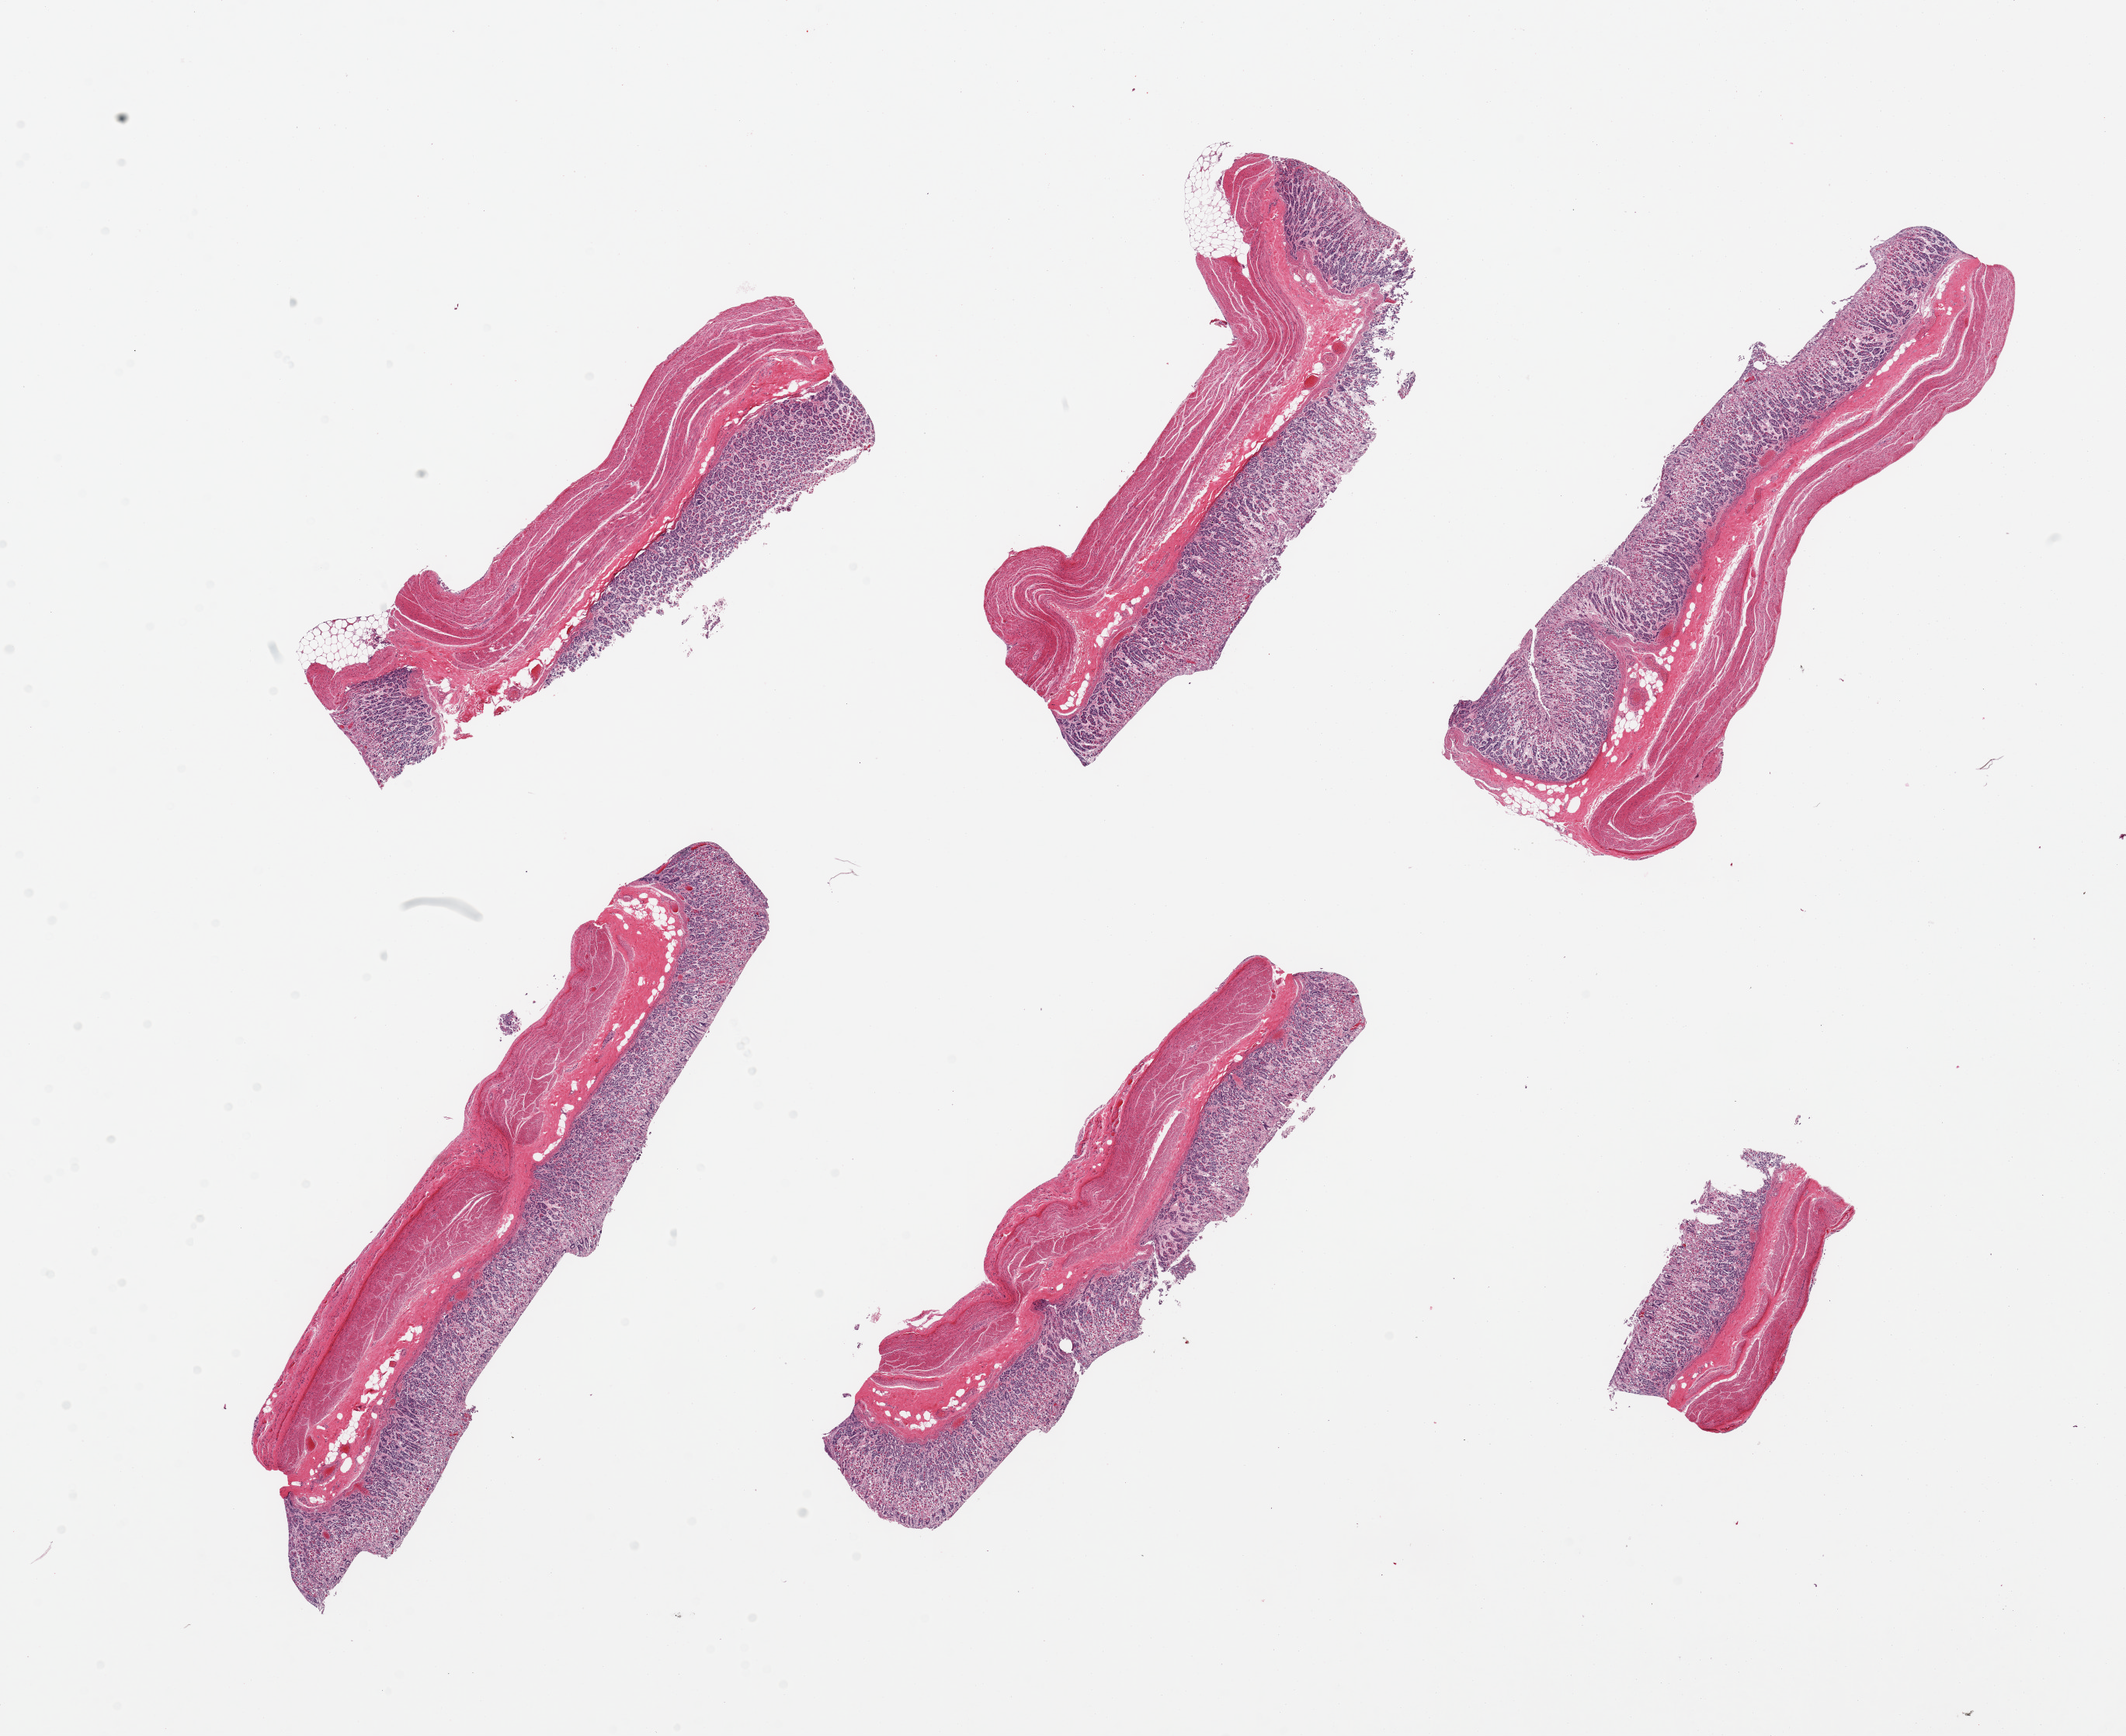
Digitized hematoxylin and eosin (H&E)-stained section, whole scanned area (about 21.7 x 17.7 mm) shown as a low-resolution overview. PAXgene-fixed, paraffin-embedded tissue. Target tissue: stomach. Tissue donor sample. Male donor.
• pathologist's review note for this sample: 6 pieces